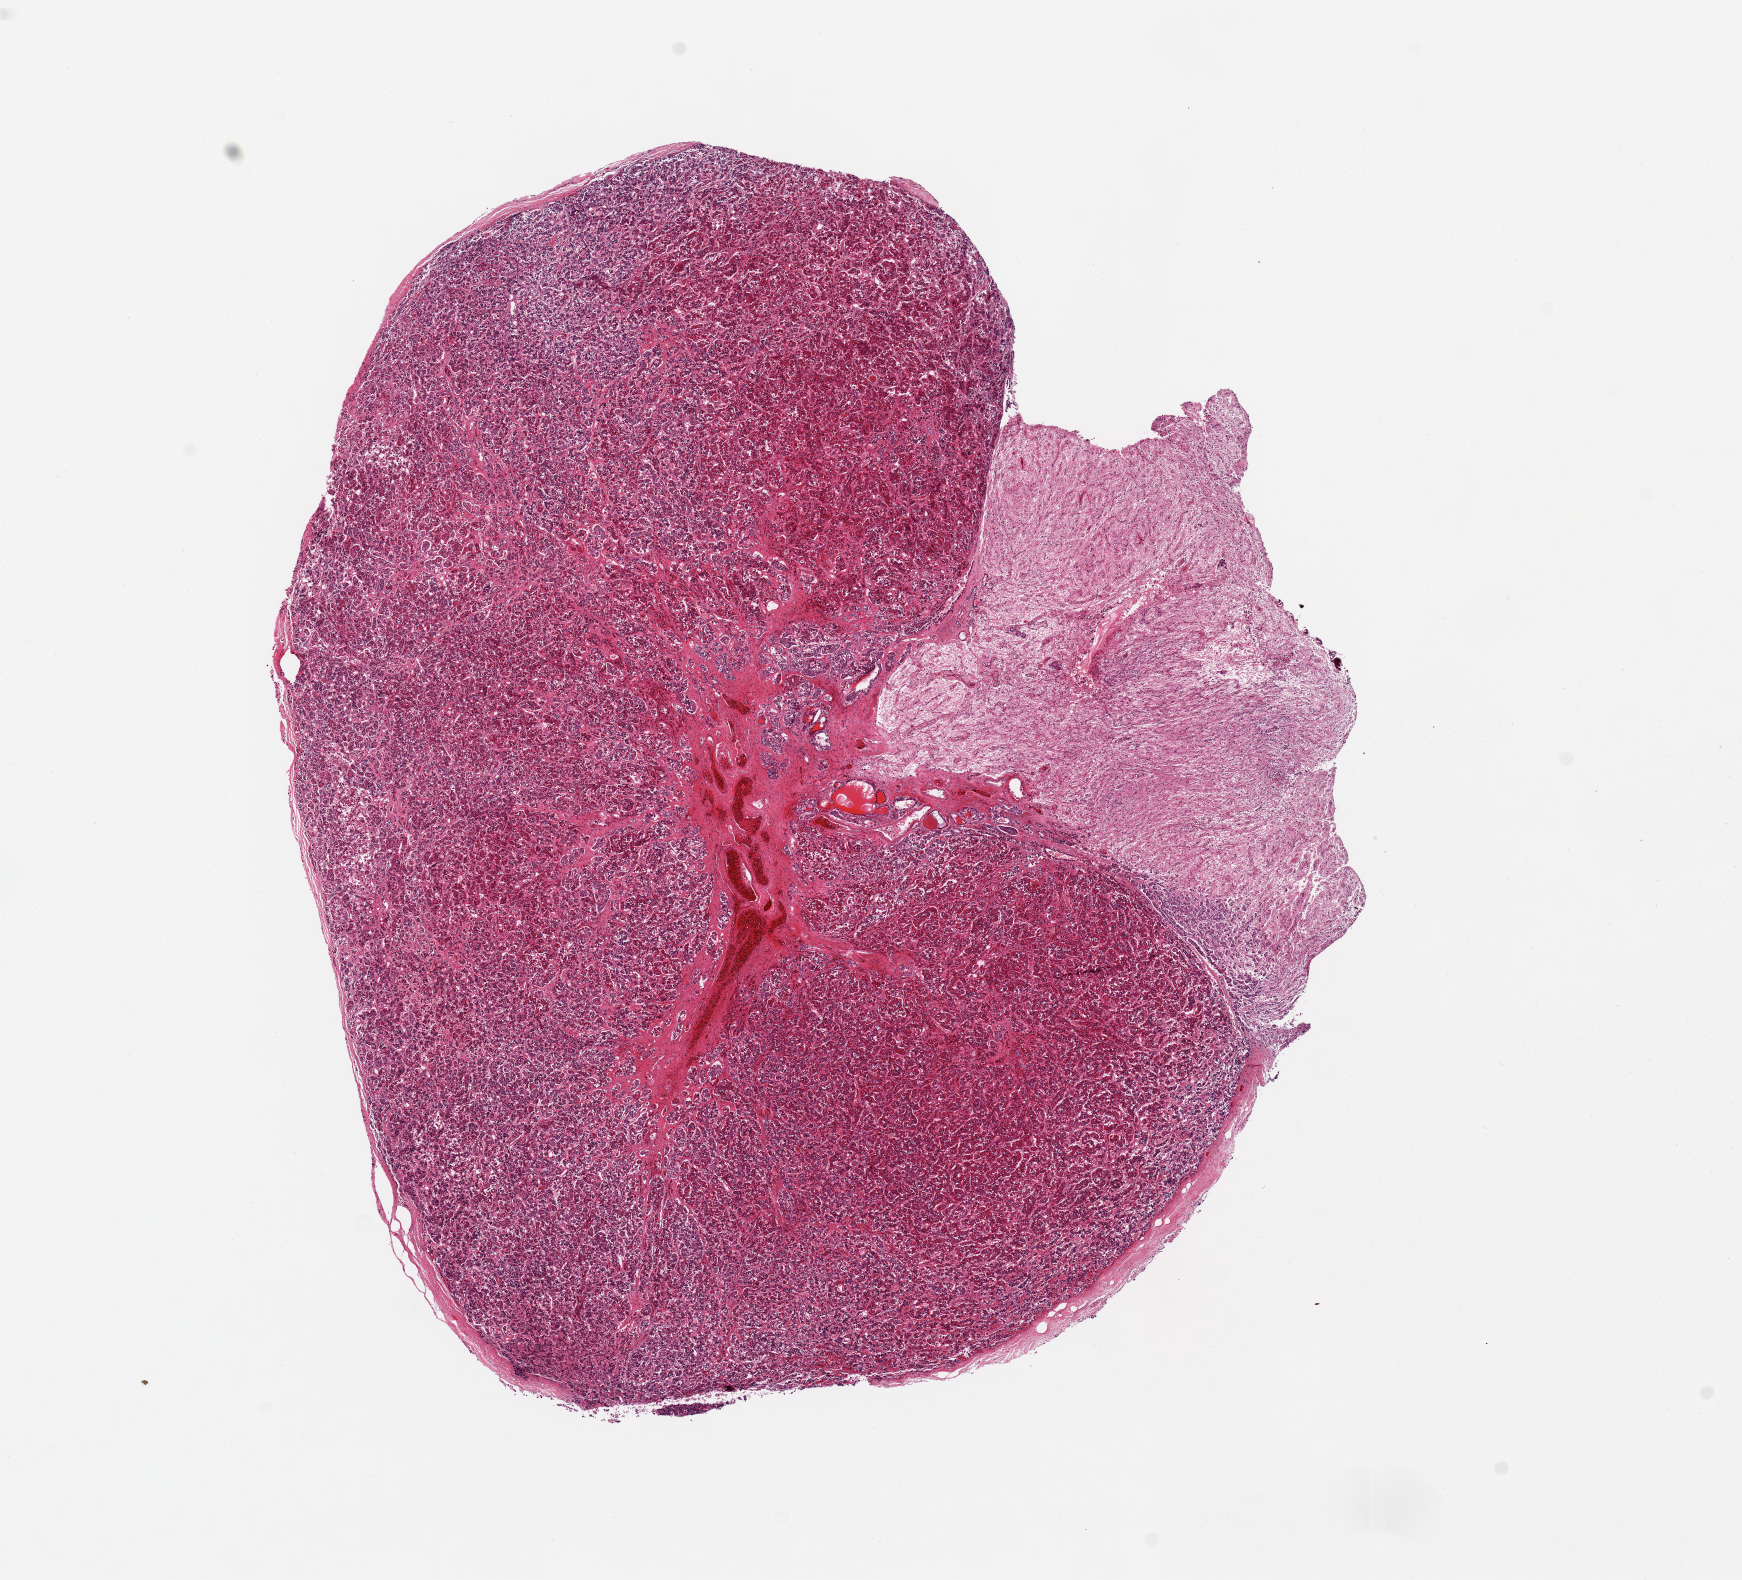
H&E whole-slide image — whole scanned area (about 13.8 x 12.5 mm, slide scanned at 20x) shown as a low-resolution overview. PAXgene-fixed, paraffin-embedded tissue. Section of pituitary (target tissue). Donor tissue sample. Male donor.
- reviewer comment on this tissue sample: 1 piece, mainly adenohypophysis, 4x3mm portion of neurohypophysis